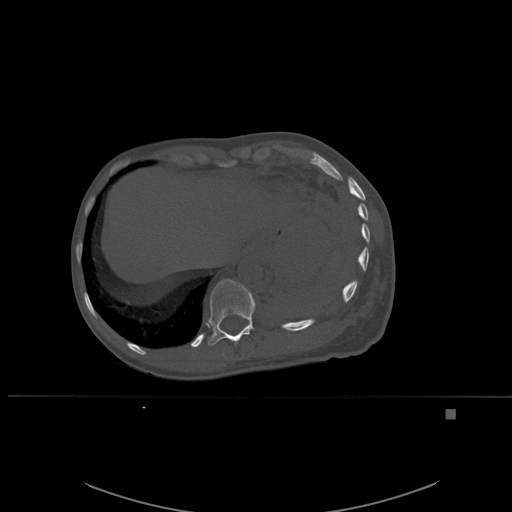
CT including the spine, one axial slice. Bone window (W 1800 / L 400 HU). 1.5 mm slice thickness. 512 × 512 image matrix, field of view 440 × 440 mm. Patient: female, 45 years. Case-level facts recorded for this patient, not image findings: primary cancer: lung.
Annotated regions visible in this slice (semi-automatically segmented with operator editing):
- T11 vertebra: bounding box (x1, y1, x2, y2) in pixels: (208, 279, 256, 346)